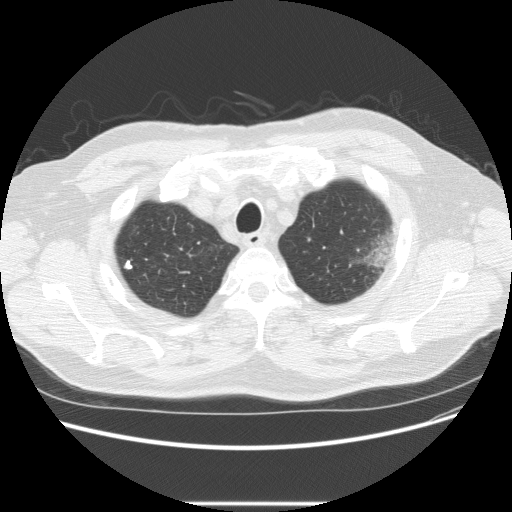
Low-dose screening chest CT, one axial slice; slice 196 of 233 in the series (ordered by position); 120 kVp; lung window (W 1500 / L -600 HU); 512 × 512 image matrix, field of view 380 × 380 mm.
Annotated regions visible in this slice (manually delineated by an expert):
- lesion 1 (tumor, upper lobe of left lung): bounding box <361,229,393,267> (left, top, right, bottom; pixels)